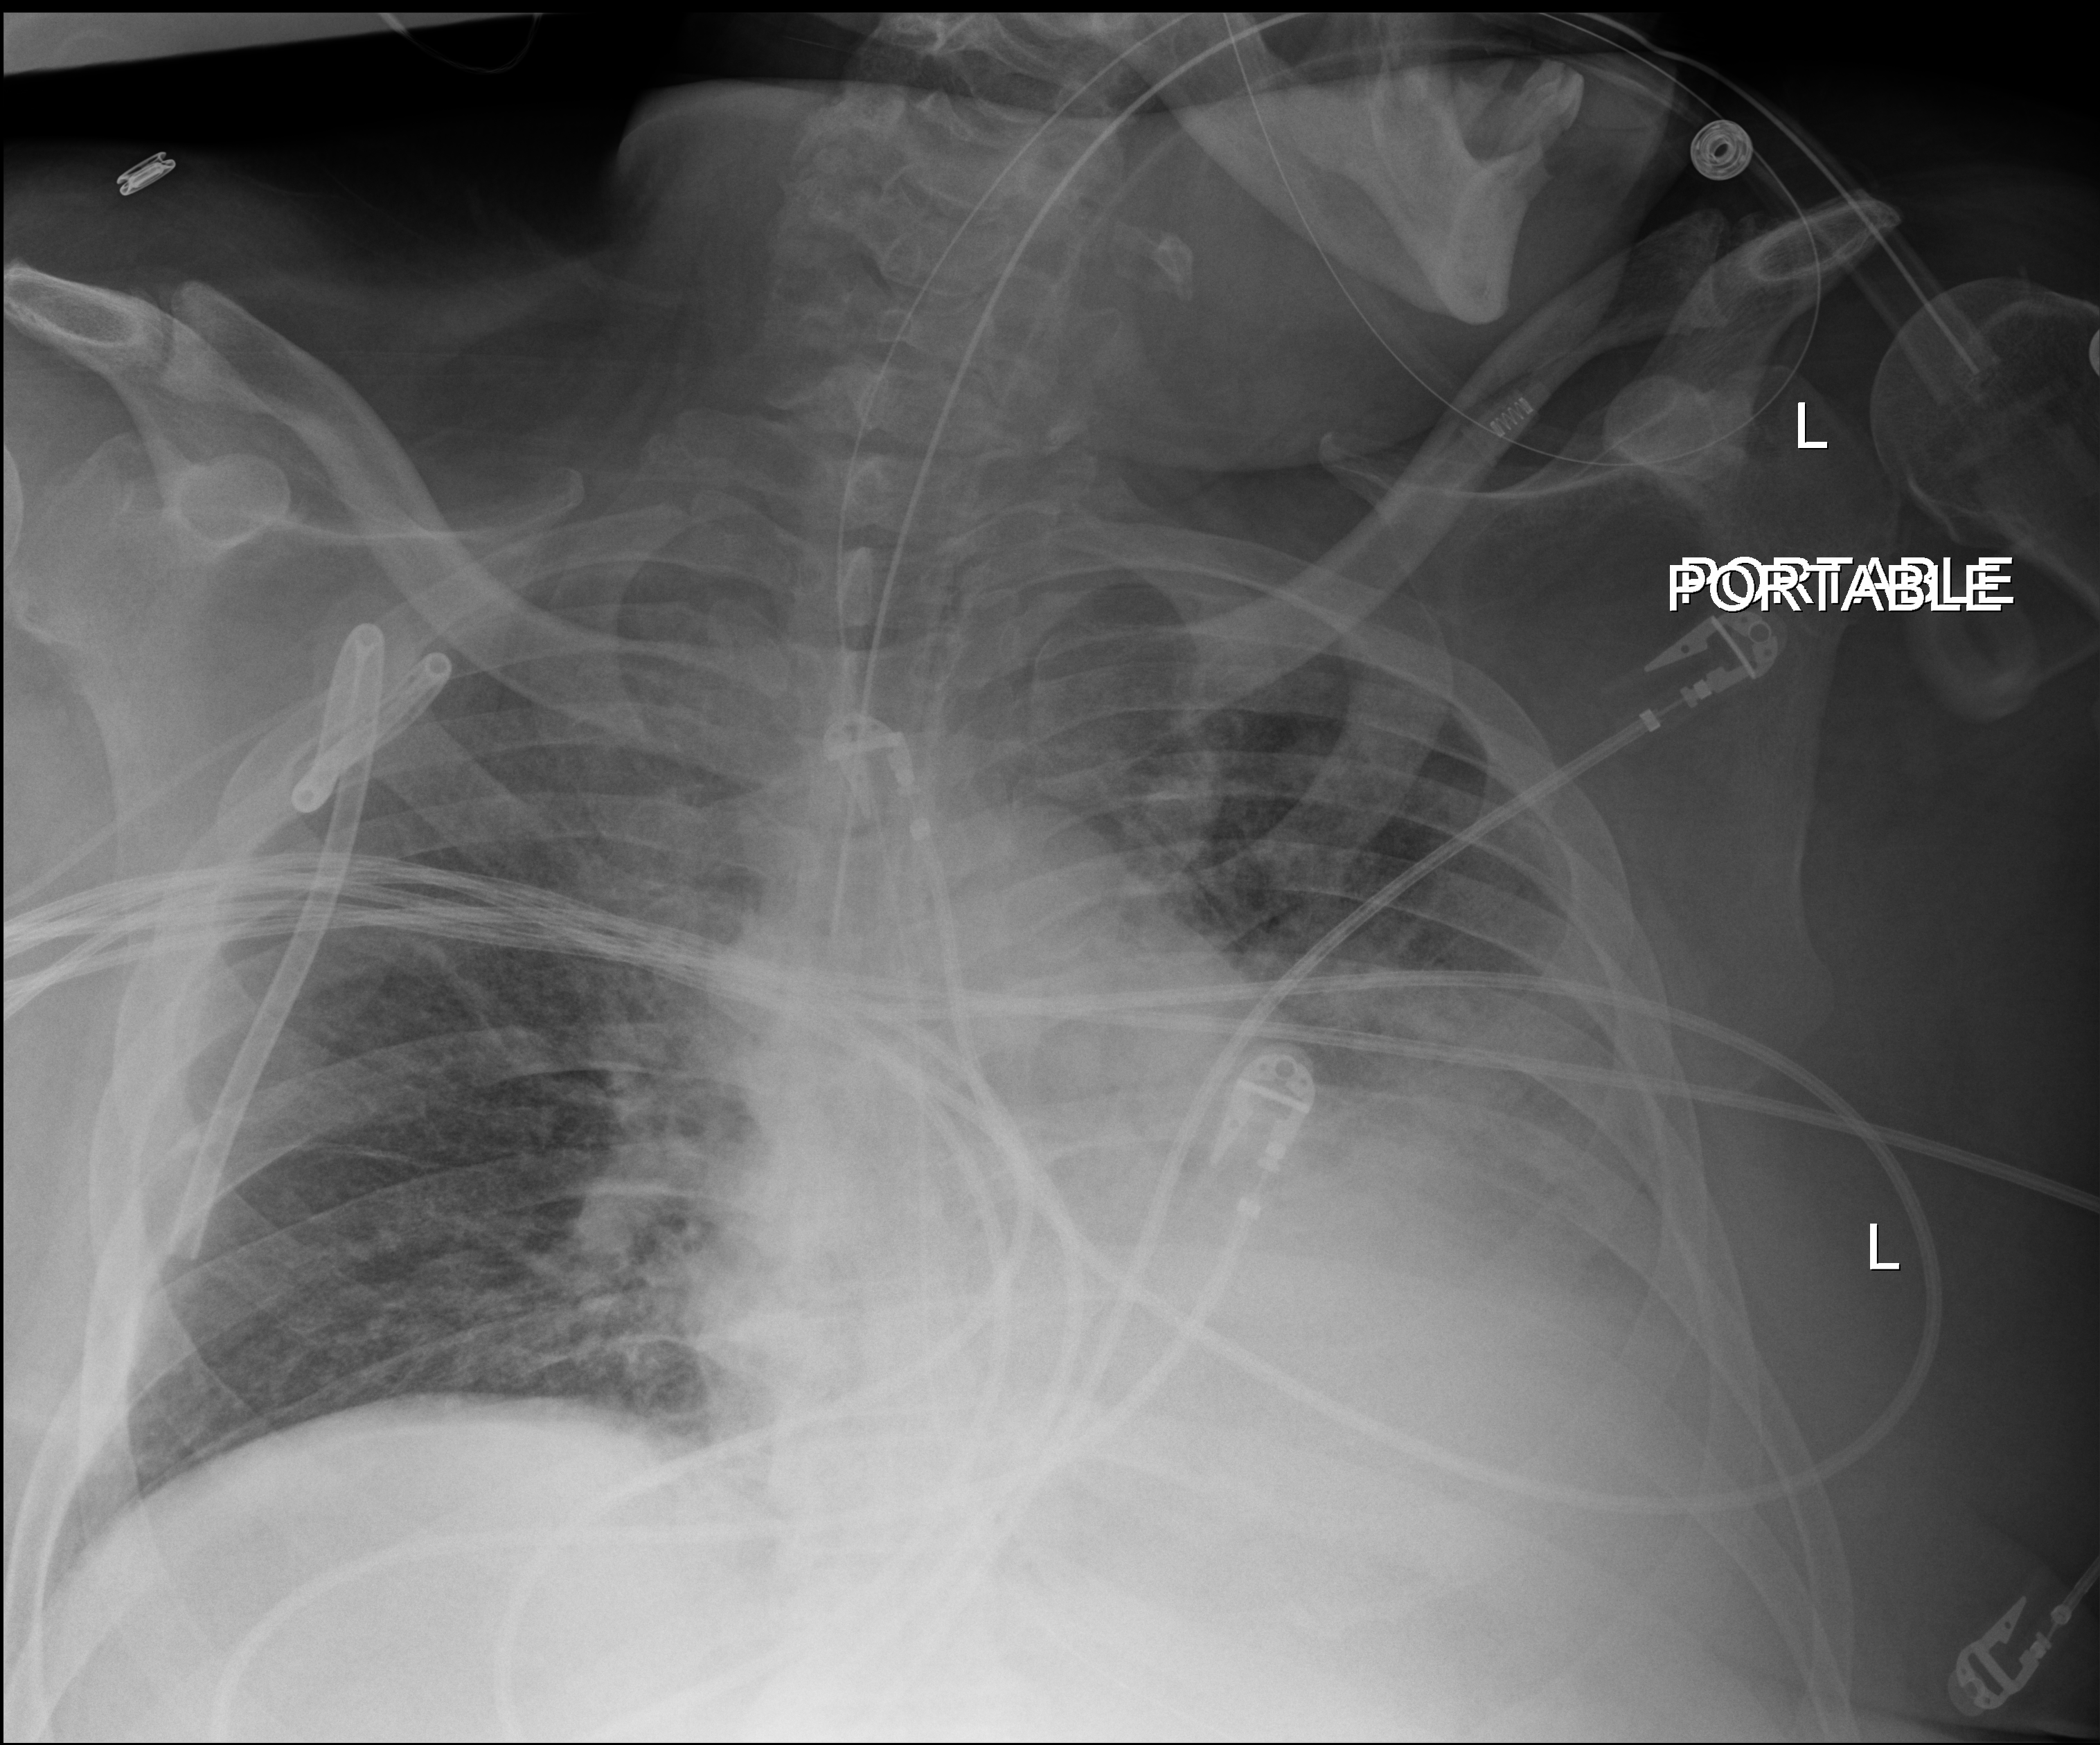
Chest radiograph, anteroposterior (AP) projection. Patient hospitalised with COVID-19; male, aged 60–74 years.
Admission-level facts for this patient (not findings on this image; timing relative to this image not recorded):
- mechanically ventilated during this hospital stay: yes
- admitted to intensive care during this hospital stay: yes